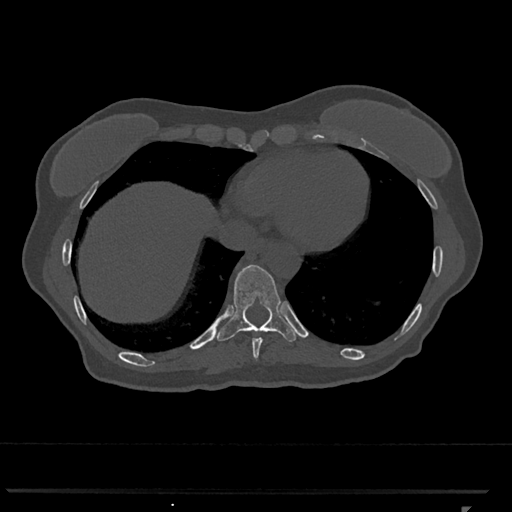
CT including the spine, one axial slice. Position 582 of 793 along the scan axis. Reconstruction kernel Br40s/3. Bone window (W 1800 / L 400 HU). 512 × 512 image matrix, field of view 380 × 380 mm. Female patient, age 62 years. From the clinical record (not read from this slice): primary cancer: renal.
Annotated regions visible in this slice (semi-automatic segmentation, software-assisted and operator-edited):
- T10 vertebra: bounding box (x1, y1, x2, y2) in pixels: (217, 264, 298, 342)
- T9 vertebra: (252, 331, 275, 360)